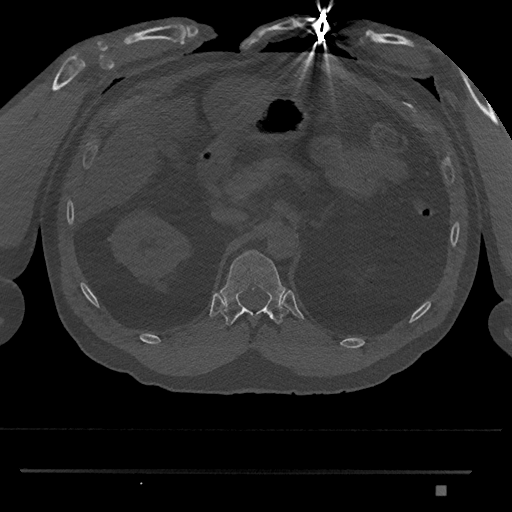
CT including the spine, one axial slice; slice 894 of 1134 in the series (ordered by position); reconstruction kernel Br40s/3; 120 kVp; bone window (W 1800 / L 400 HU); 512 × 512 image matrix, field of view 429 × 429 mm. Male patient, age 65 years. Case-level facts recorded for this patient, not image findings: primary cancer: prostate.
Structures marked on this image (semi-automatic segmentation, software-assisted and operator-edited):
- T12 vertebra: bounding box [x1, y1, x2, y2] px = [220, 250, 289, 327]